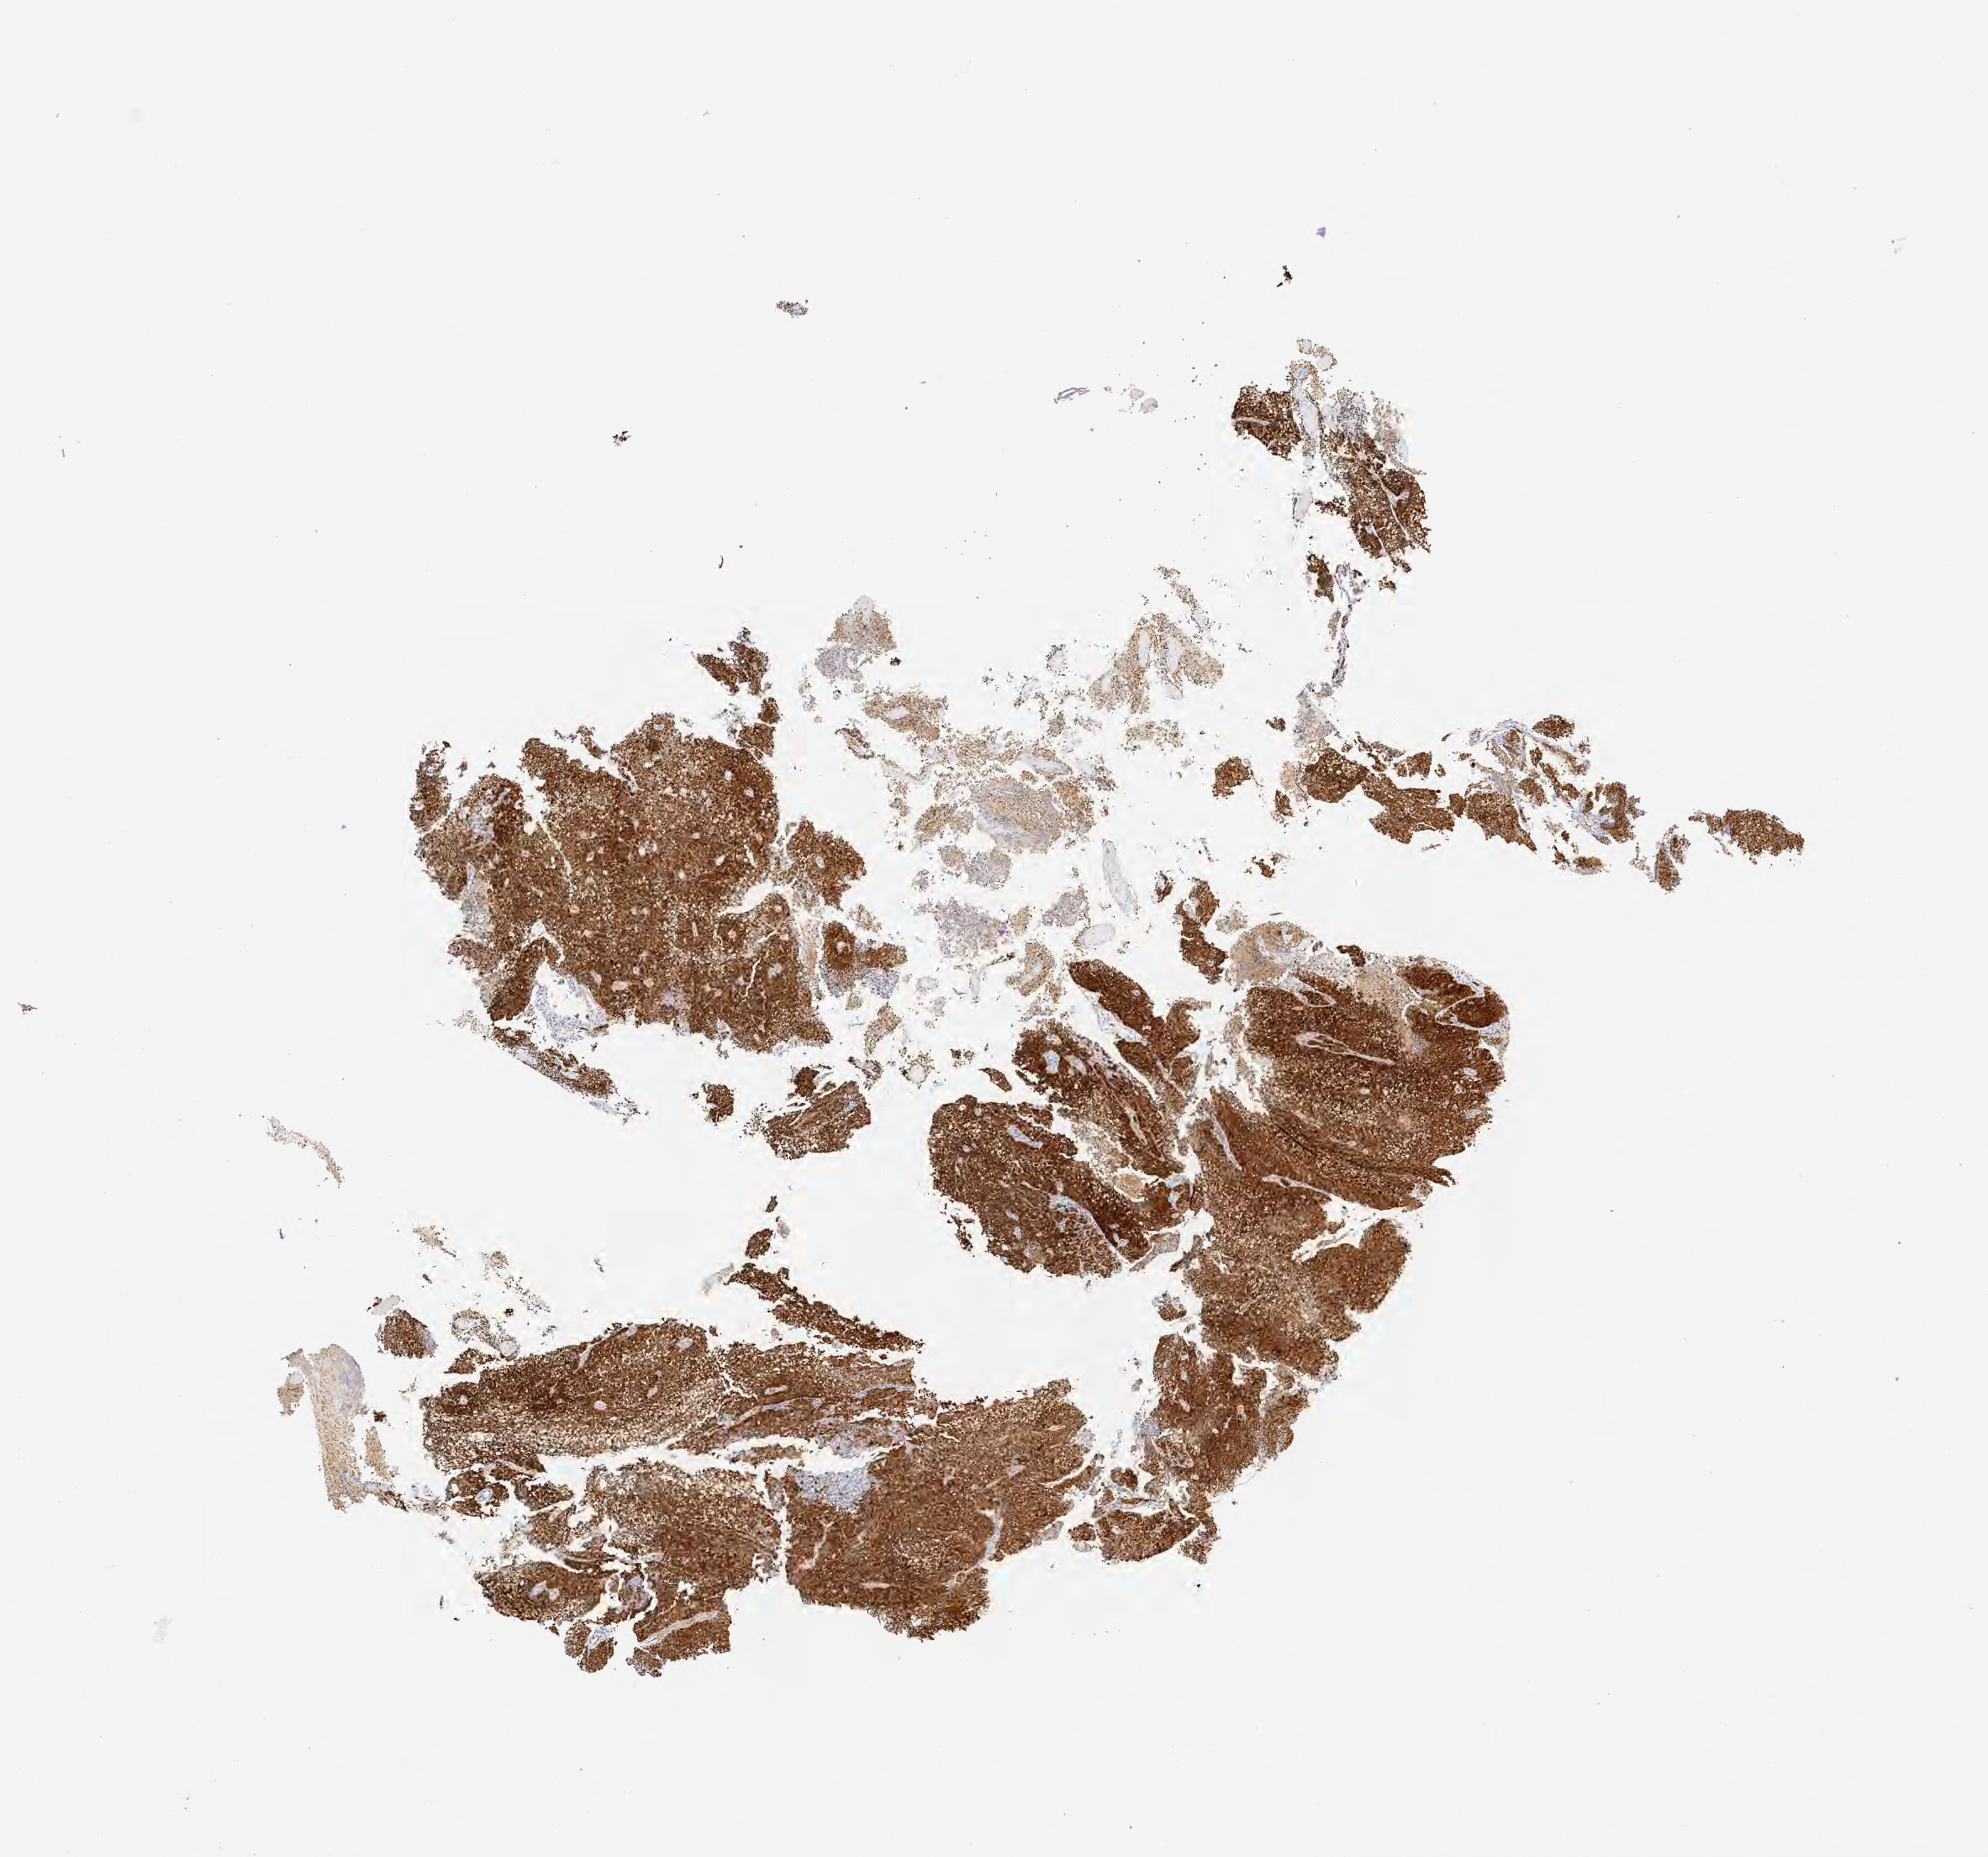
IHC for p16 (p16INK4a), whole-slide image, shown as a low-resolution overview of the whole scanned area (about 9.6 x 8.9 mm). Specimen: tumor tissue. Anatomic site: cervix. Female patient, aged 30.
Diagnosis: Squamous cell carcinoma, large cell, nonkeratinizing, NOS.